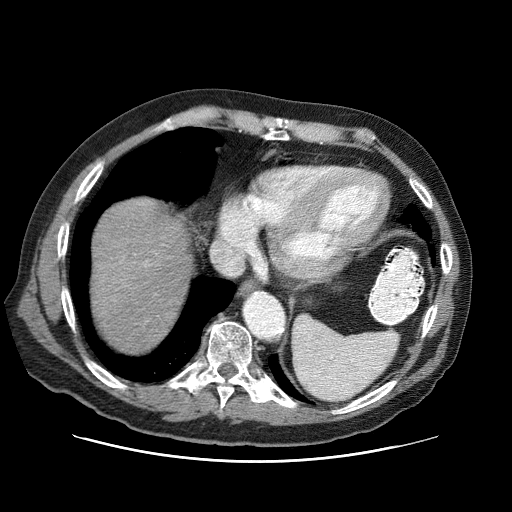
Contrast-enhanced abdominal CT (liver protocol), one axial slice. Slice 68 of 87 in the series (ordered by position). Reconstruction kernel STANDARD. 120 kVp. One of 3 acquisitions stored at this slice position. Soft-tissue window (W 400 / L 40 HU). 2.5 mm slice thickness. 512 × 512 image matrix, field of view 400 × 400 mm. From the clinical record (not read from this slice): diagnosis: hepatocellular carcinoma (patient treated with transarterial chemoembolisation; whether this scan precedes or follows treatment is not stated here); TNM stage (as recorded): Stage-IIIA; Child-Pugh class: A; tumour differentiation: well differentiated; tumour nodularity: multinodular.
Annotated regions visible in this slice (semi-automatically segmented with operator editing):
- liver parenchyma outside the tumour (the mass and vessels are separate outlines, so this box may not span the whole liver): bounding box [x1, y1, x2, y2] px = [92, 198, 192, 352]